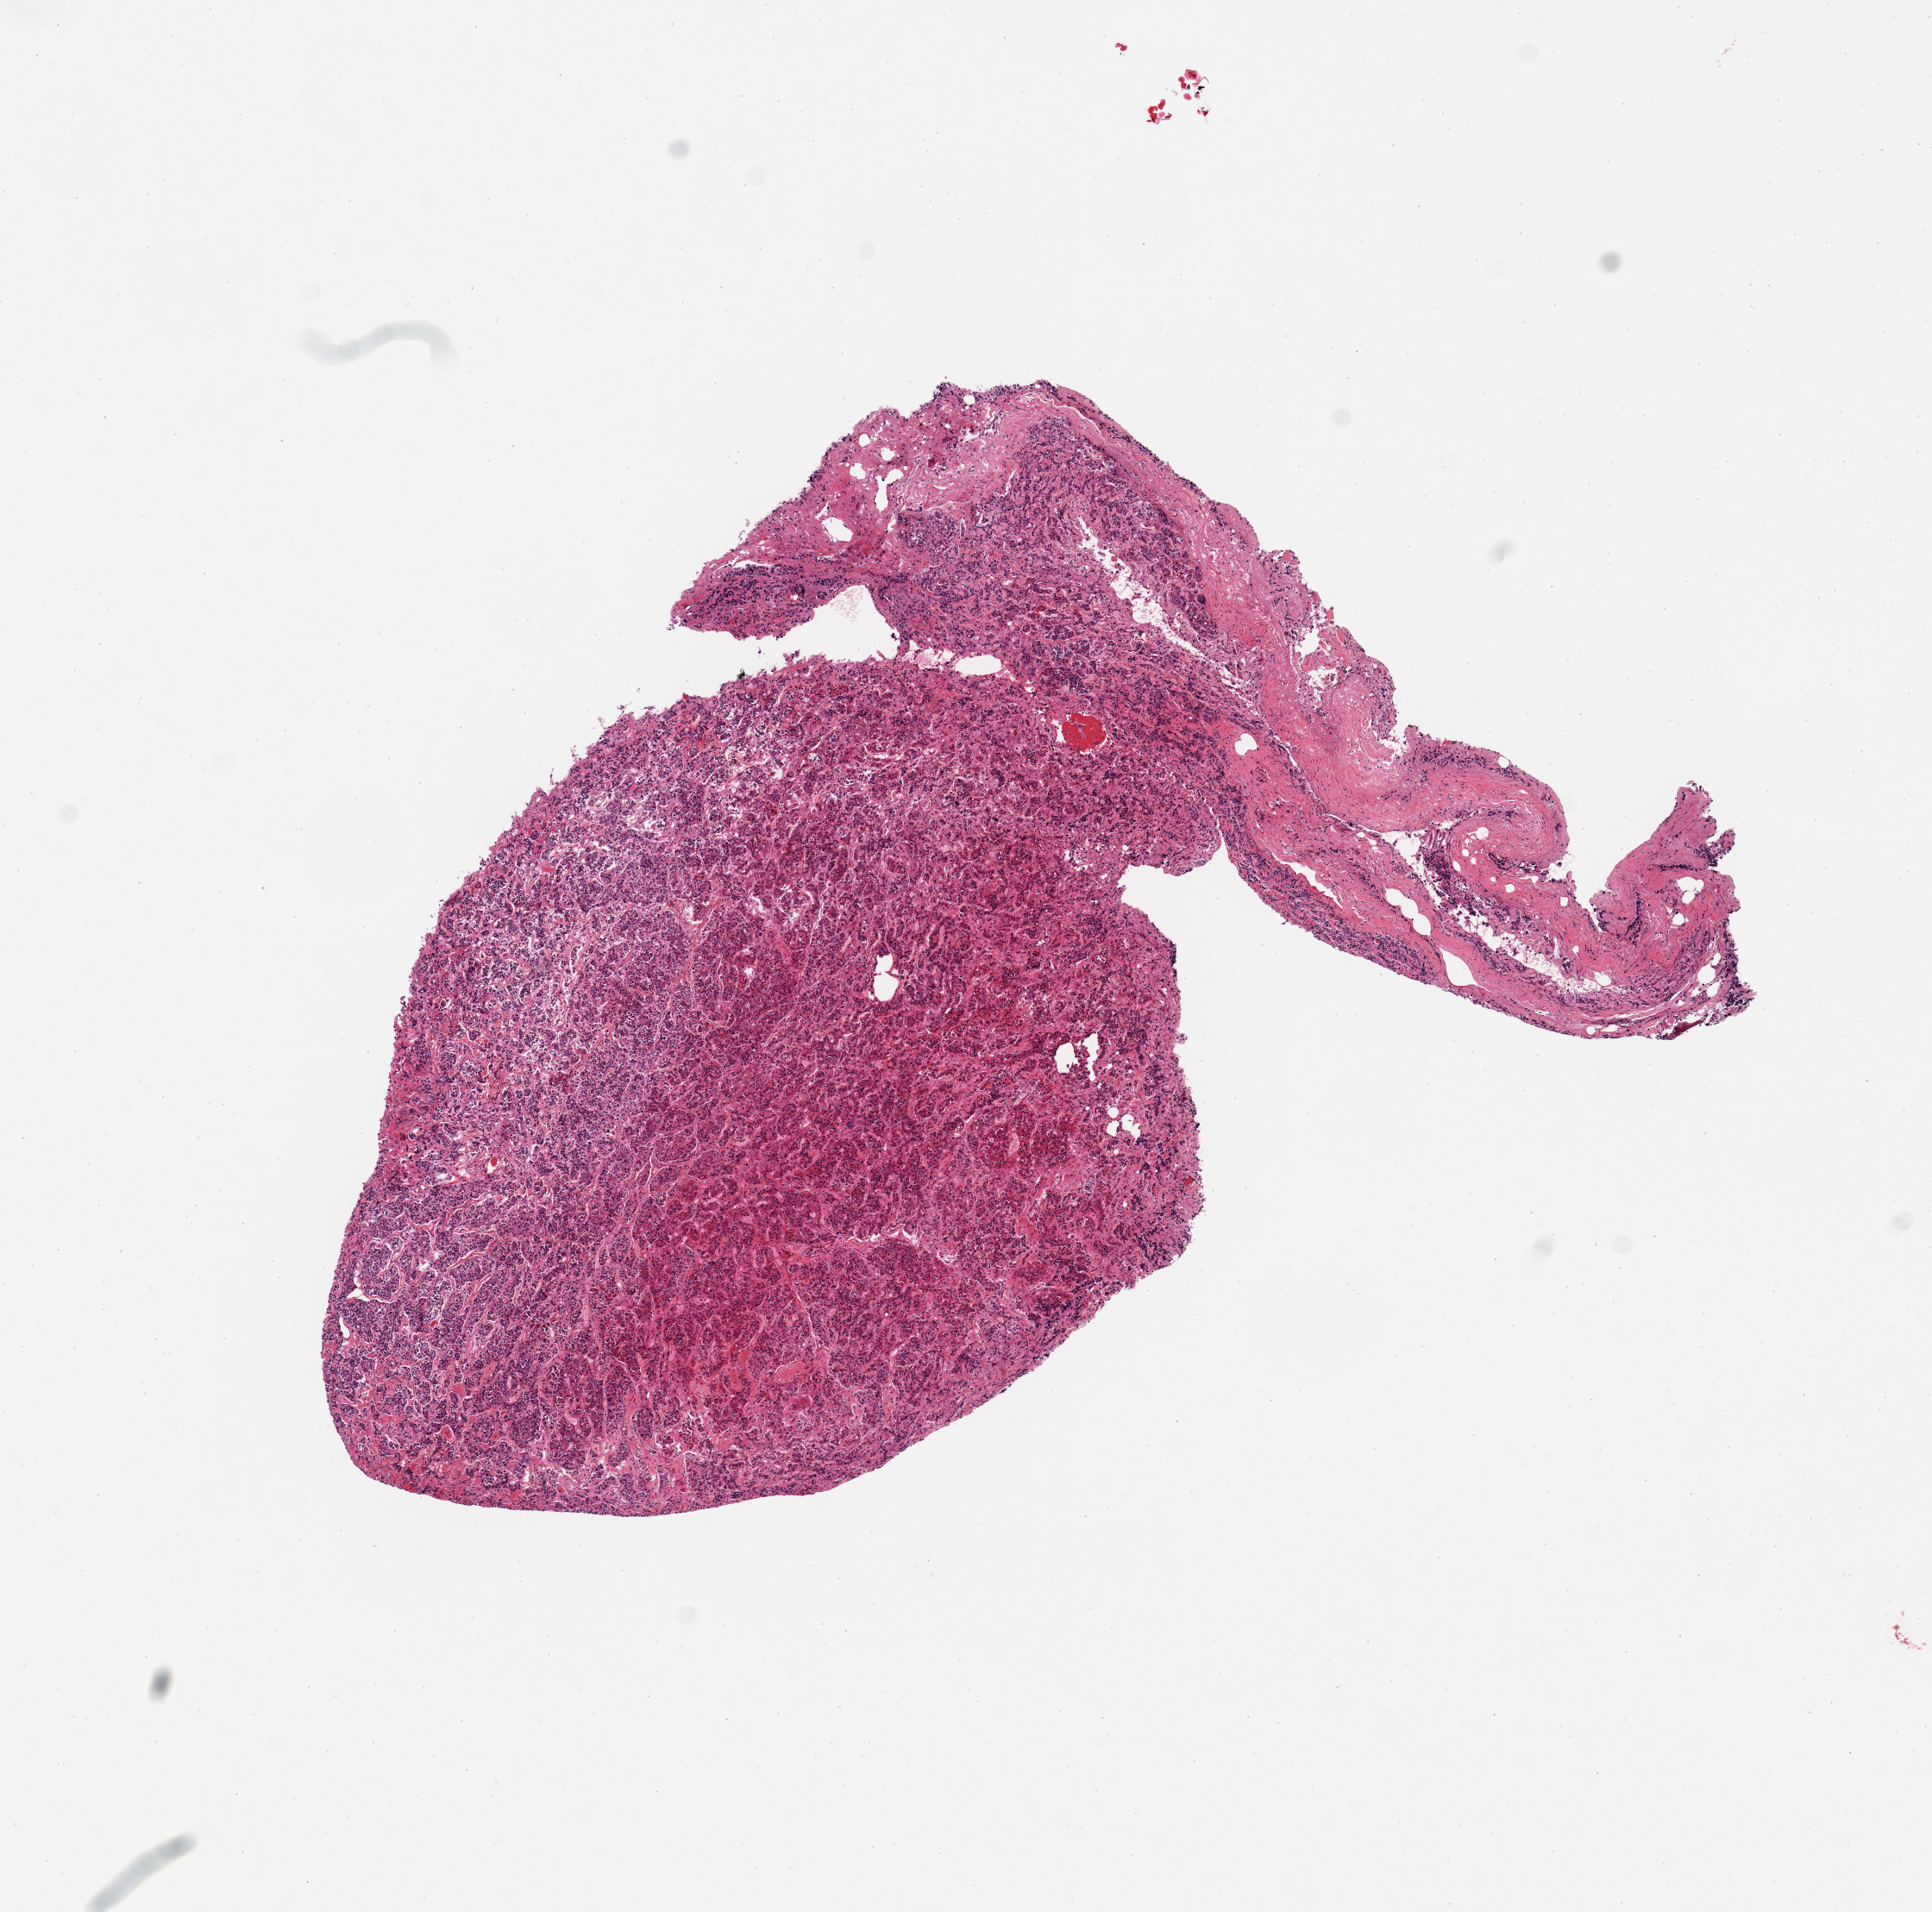
Haematoxylin and eosin whole-slide image — a low-resolution overview of the entire scanned area, about 8.9 x 8.8 mm (from a 20x scan); PAXgene-fixed paraffin-embedded (PFPE) section; target tissue: pituitary; donor tissue sample. Donor: male.
* review note (as recorded): 1 piece; adenohypophysis and dura